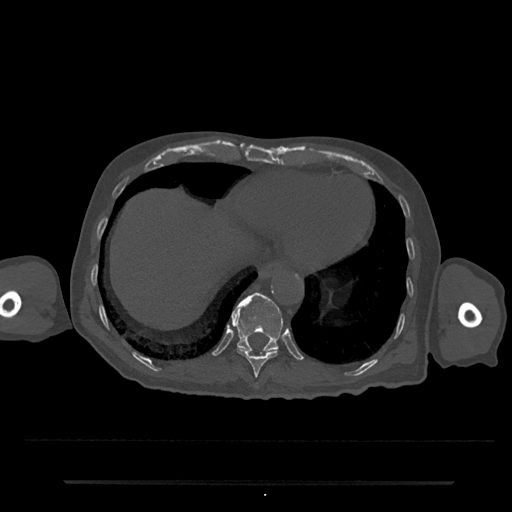
CT including the spine, one axial slice; slice 287 of 797 in the series (ordered by position); 120 kVp; bone window (W 1800 / L 400 HU); 0.5 mm slice thickness; 512 × 512 image matrix, field of view 427 × 427 mm. Male patient, age 74 years. From the clinical record (not read from this slice): primary cancer: prostate.
Outlined on this slice (semi-automatic segmentation, software-assisted and operator-edited):
- T10 vertebra: bounding box [x1, y1, x2, y2] px = [237, 348, 278, 385]
- T11 vertebra: [231, 292, 283, 354]